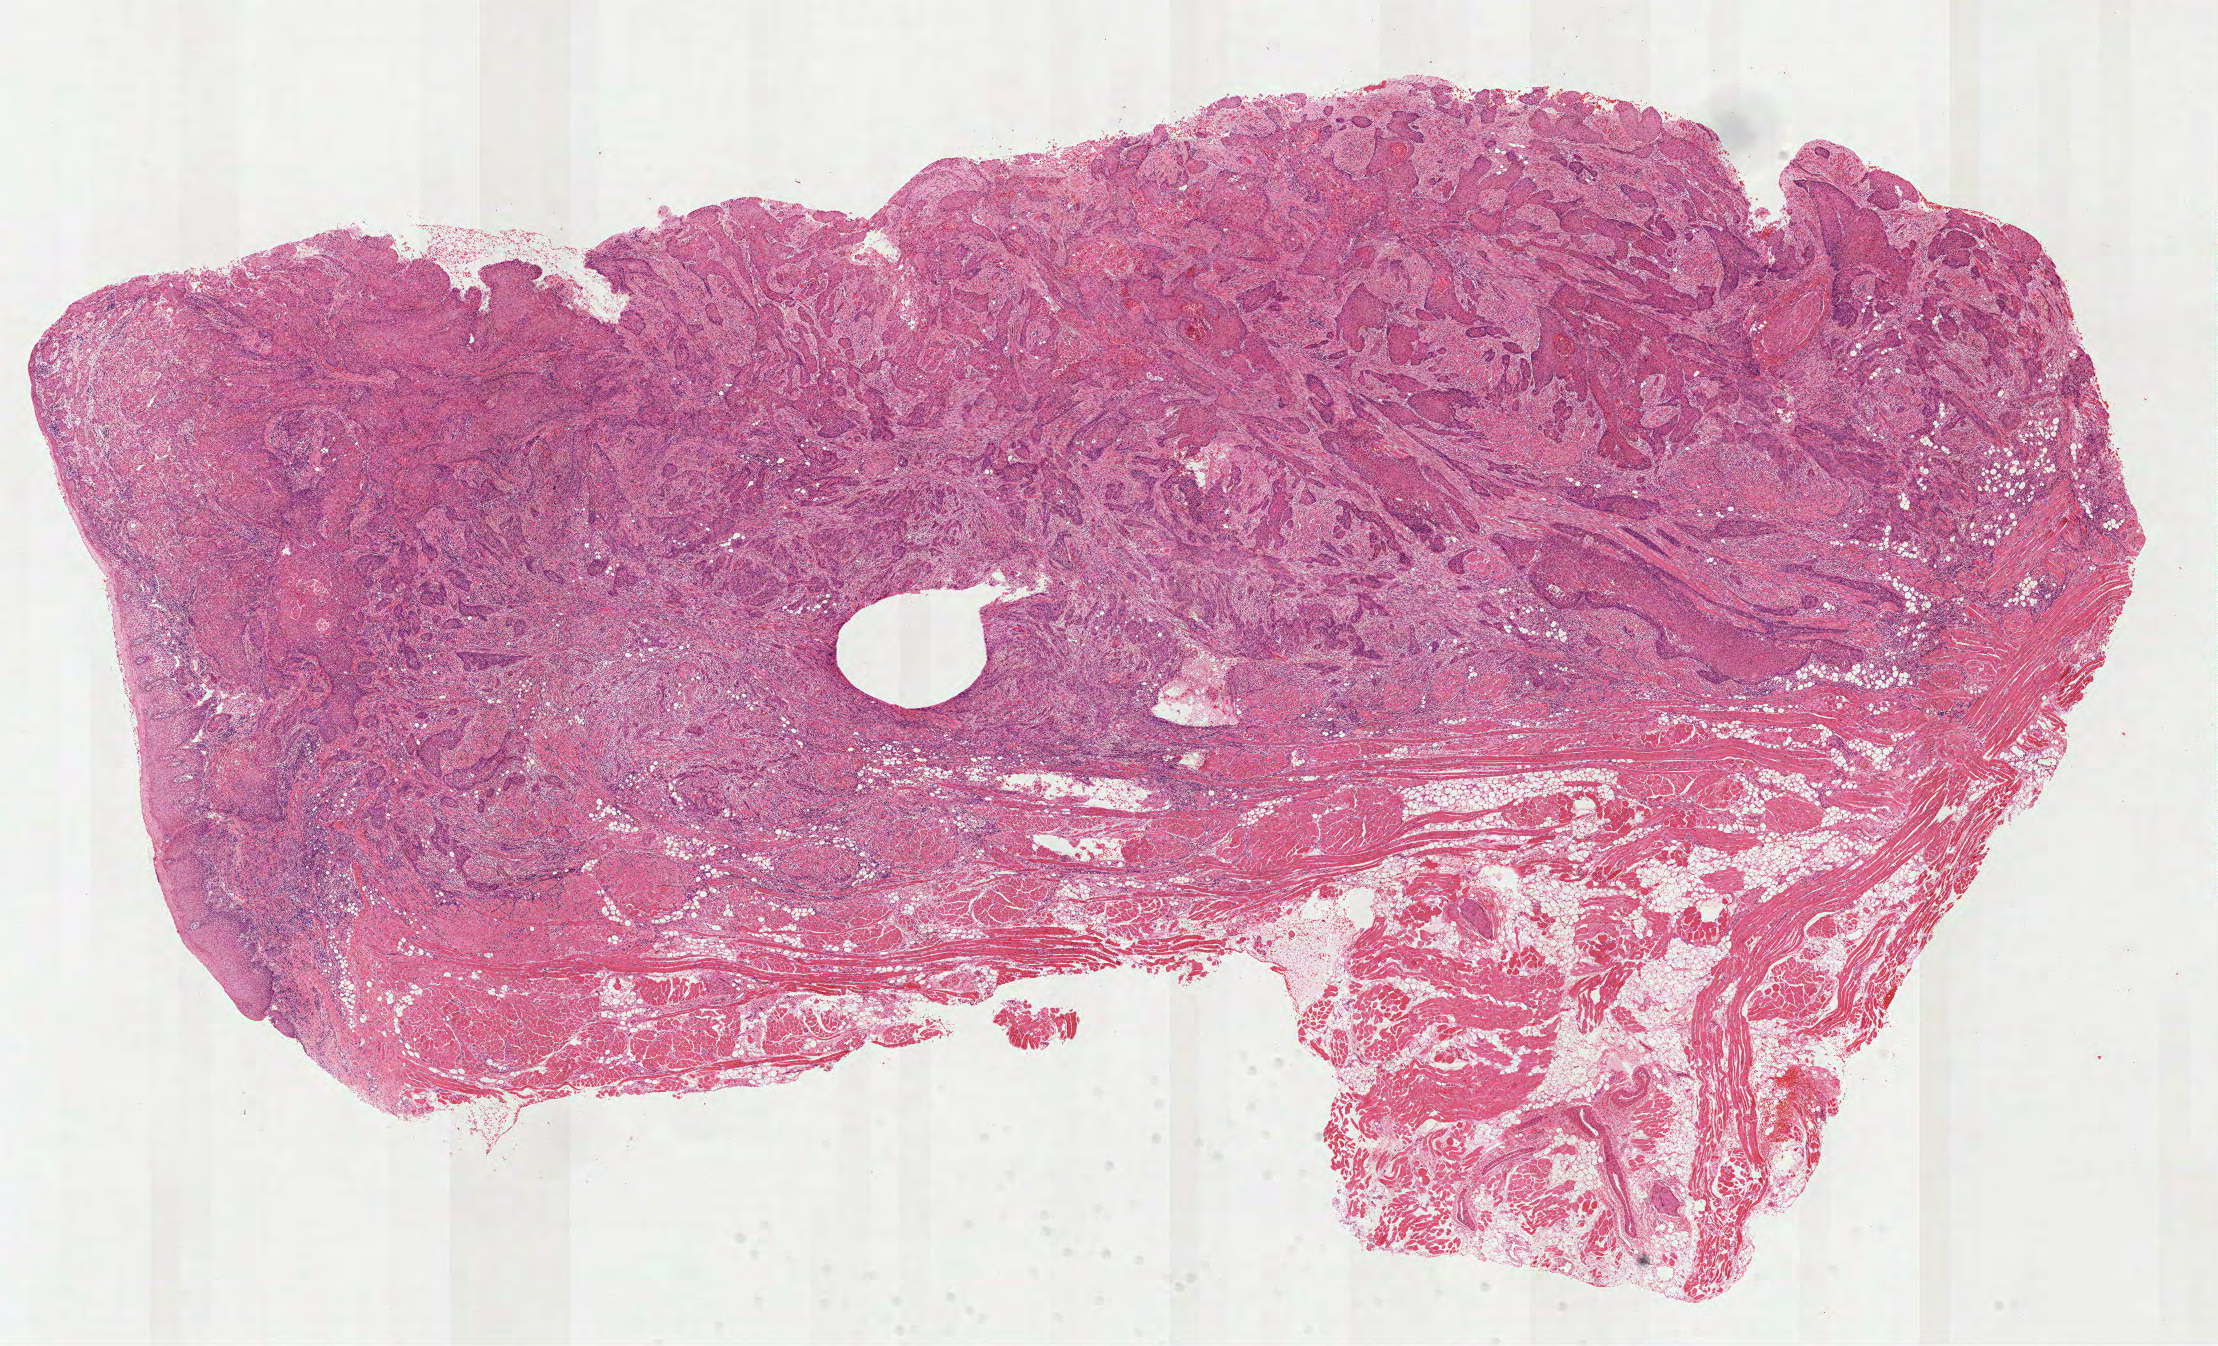
H&E-stained whole-slide image — shown as a low-resolution overview of the whole scanned area (about 17.9 x 10.9 mm, slide scanned at 40x); formalin-fixed paraffin-embedded (FFPE) diagnostic section; sample: primary tumour, head and neck. Patient: male, age at initial diagnosis 48 years.
Pathologic diagnosis: Squamous cell carcinoma, NOS (floor of mouth, NOS).